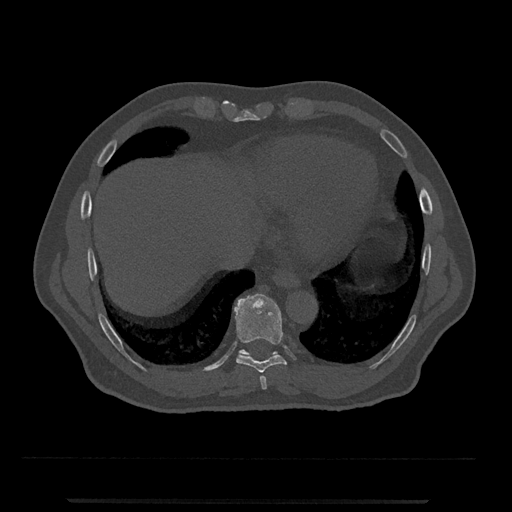
CT including the spine, one axial slice. Slice 564 of 797 in the series (ordered by position). 120 kVp. Bone window (W 1800 / L 400 HU). 0.5 mm slice thickness. 512 × 512 image matrix, field of view 419 × 419 mm. Male patient, age 63 years. Case-level facts recorded for this patient, not image findings: primary cancer: prostate.
Annotated regions visible in this slice (semi-automatic segmentation, software-assisted and operator-edited):
- T10 vertebra: bounding box (x1, y1, x2, y2) in pixels: (239, 349, 278, 356)
- T8 vertebra: (260, 376, 267, 390)
- T9 vertebra: (234, 293, 287, 373)